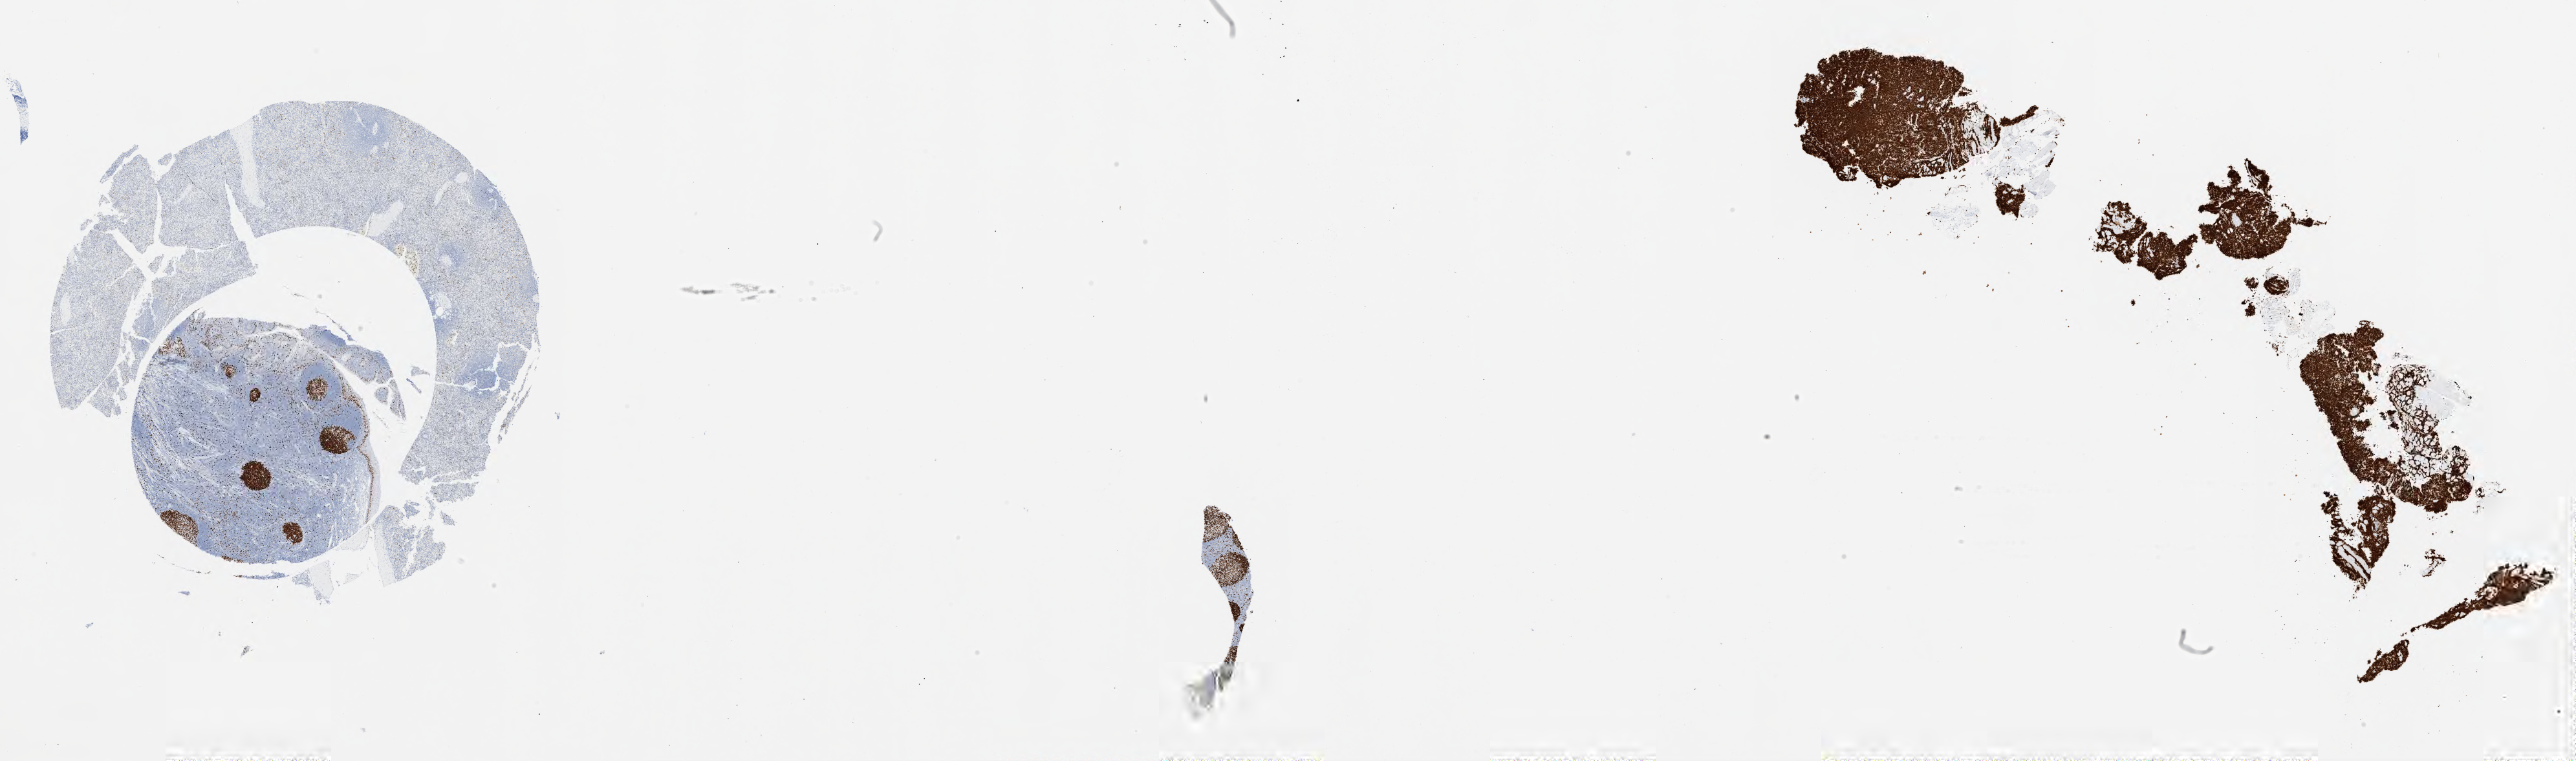
Immunohistochemistry (IHC) whole-slide image stained for Ki-67, shown as a low-resolution overview of the whole scanned area (about 32.0 x 9.5 mm), specimen: tumor tissue. Patient female; aged 69.
Histologic diagnosis: Burkitt lymphoma, NOS.